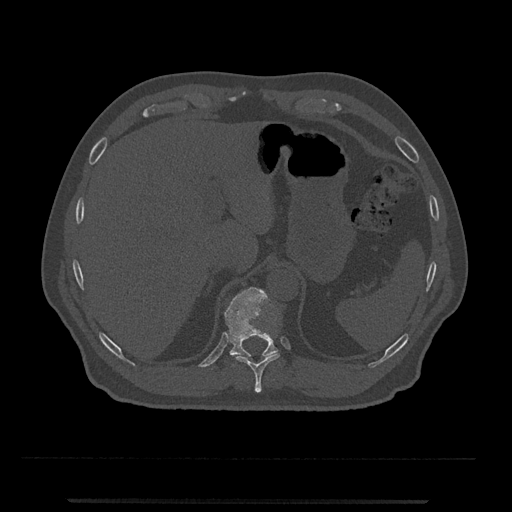
CT including the spine, one axial slice. Bone window (W 1800 / L 400 HU). 0.5 mm slice thickness. 512 × 512 image matrix, field of view 419 × 419 mm. Male patient, age 63 years. From the clinical record (not read from this slice): primary cancer: prostate.
Annotated regions visible in this slice (semi-automatically segmented with operator editing):
- T10 vertebra: bounding box <236,352,280,393> (left, top, right, bottom; pixels)
- T11 vertebra: <225,287,278,366>